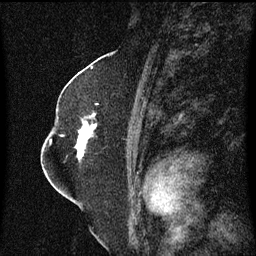
Breast MRI (dynamic contrast-enhanced), one sagittal slice. Position 36 of 60 along the scan axis. Dynamic contrast-enhanced series, image 2 of 3 at this slice position (ordered by acquisition). 1.5 T. TE 4.2 ms, TR 8.4 ms. 256 × 256 image matrix. Female patient, age 52 years. From the clinical record (not read from this slice): setting: breast cancer imaged before/during neoadjuvant chemotherapy; receptor status: HR-positive, HER2-negative.
Structures marked on this image (semi-automatic segmentation, software-assisted and operator-edited):
- analysis volume of interest (the breast-tissue region the enhancement analysis was run in; not a lesion): bounding box [x1, y1, x2, y2] px = [64, 110, 98, 161]
- tumour enhancement mask (voxels above the 70 % enhancement threshold inside the analysis volume of interest): [76, 114, 98, 159]